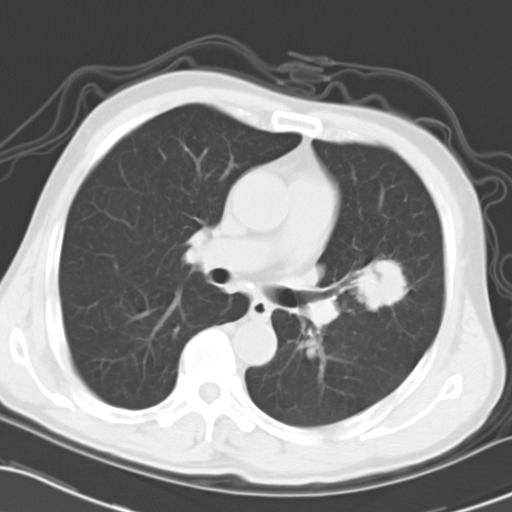
Chest CT, one axial slice. Reconstruction kernel B40f. Lung window (W 1500 / L -600 HU). 10 mm slice thickness. 512 × 512 image matrix. Male patient, age 60 years. Case-level facts recorded for this patient, not image findings: clinical TNM (as recorded): T1c N1 M0.
Outlined on this slice (bounding box drawn by a radiologist):
- lung tumour (recorded histology: adenocarcinoma): bounding box [x1, y1, x2, y2] px = [353, 258, 408, 312]
- lung tumour (recorded histology: adenocarcinoma): [357, 258, 404, 318]